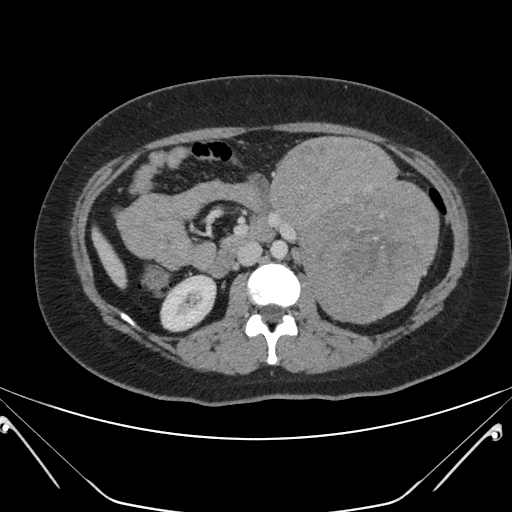
Contrast-enhanced abdominal CT, one axial slice. Position 105 of 168 along the scan axis. Intravenous contrast given. Soft-tissue window (W 400 / L 40 HU). 512 × 512 image matrix. Female patient, age 26 years. Case-level facts recorded for this patient, not image findings: diagnosis: adrenocortical carcinoma; tumour side: left adrenal; tumour size at pathology: 28 cm; Ki-67 index: 20 %; stage (as recorded): 2.
Structures marked on this image (semi-automatically segmented with operator editing):
- mass: bounding box [x1, y1, x2, y2] px = [269, 136, 439, 324]